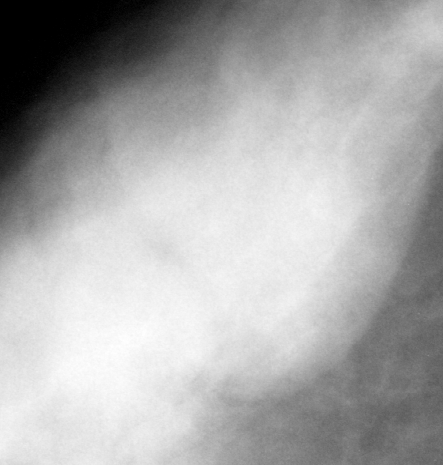
Cropped region of a digitized screen-film mammogram centred on a radiologist-marked abnormality; right breast; CC view; BI-RADS breast density category 3 (scale 1–4).
Mass, shape lobulated, margins ill defined; BI-RADS assessment category 3; pathology result (as recorded, not read from the image): benign.